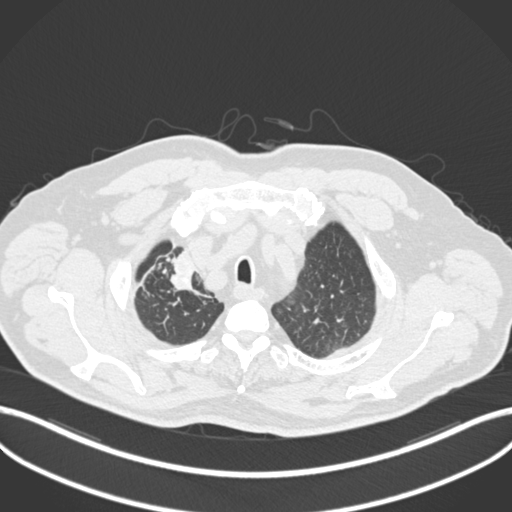
Chest CT, one axial slice. Position 174 of 255 along the scan axis. Reconstruction kernel B30f. 120 kVp. Lung window (W 1500 / L -600 HU). 512 × 512 image matrix, field of view 400 × 400 mm. Patient: male, 60 years. Case-level facts recorded for this patient, not image findings: clinical TNM (as recorded): T1b N1 M0.
Outlined on this slice (rectangle marked by the reading radiologist):
- lung tumour (recorded histology: squamous cell carcinoma): bounding box [x1, y1, x2, y2] px = [159, 243, 205, 296]